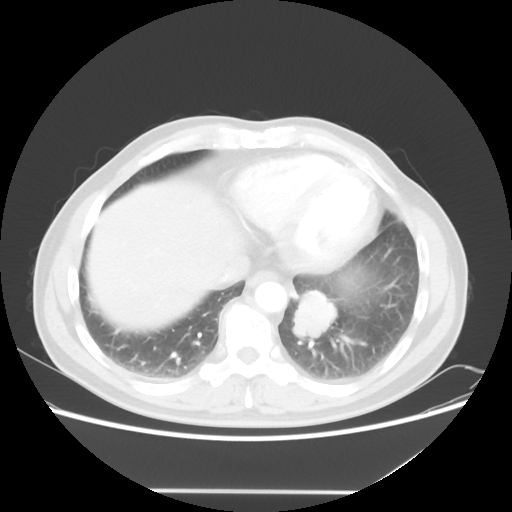
Chest CT, one axial slice. Position 17 of 56 along the scan axis. Lung window (W 1500 / L -600 HU). 5 mm slice thickness. 512 × 512 image matrix, field of view 385 × 385 mm. Male patient, age 61 years. Case-level facts recorded for this patient, not image findings: clinical TNM (as recorded): T1c N0 M0; histopathological grade: G3.
Annotated regions visible in this slice (rectangle marked by the reading radiologist):
- lung tumour (recorded histology: adenocarcinoma): bounding box <290,284,347,347> (left, top, right, bottom; pixels)